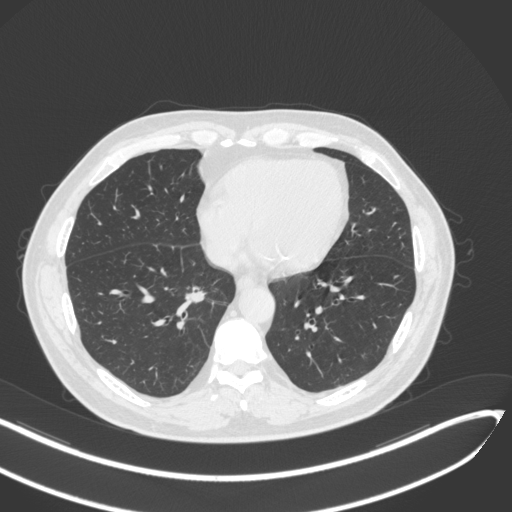
Chest CT, one axial slice; slice 135 of 429 in the series (ordered by position); lung window (W 1500 / L -600 HU); 512 × 512 image matrix. Patient: male, 62 years. From the clinical record (not read from this slice): clinical TNM (as recorded): T1b N0 M0.
Annotated regions visible in this slice (bounding box drawn by a radiologist):
- lung tumour (recorded histology: adenocarcinoma): bounding box (x1, y1, x2, y2) in pixels: (183, 286, 212, 306)